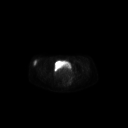
FDG PET of an extremity soft-tissue mass (from a PET/CT study), one axial slice; slice 71 of 267 in the series (ordered by position); 3.27 mm slice thickness; 128 × 128 image matrix, field of view 700 × 700 mm. Patient: female, 34 years. From the clinical record (not read from this slice): histological type: synovial sarcoma; grade: intermediate; site of the primary tumour: right thigh.
Outlined on this slice (expert contour drawn on MRI and transferred to this co-registered scan by the dataset authors):
- gross tumour volume including surrounding oedema: bounding box <33,59,38,66> (left, top, right, bottom; pixels)
- gross tumour volume (mass): <33,59,37,66>